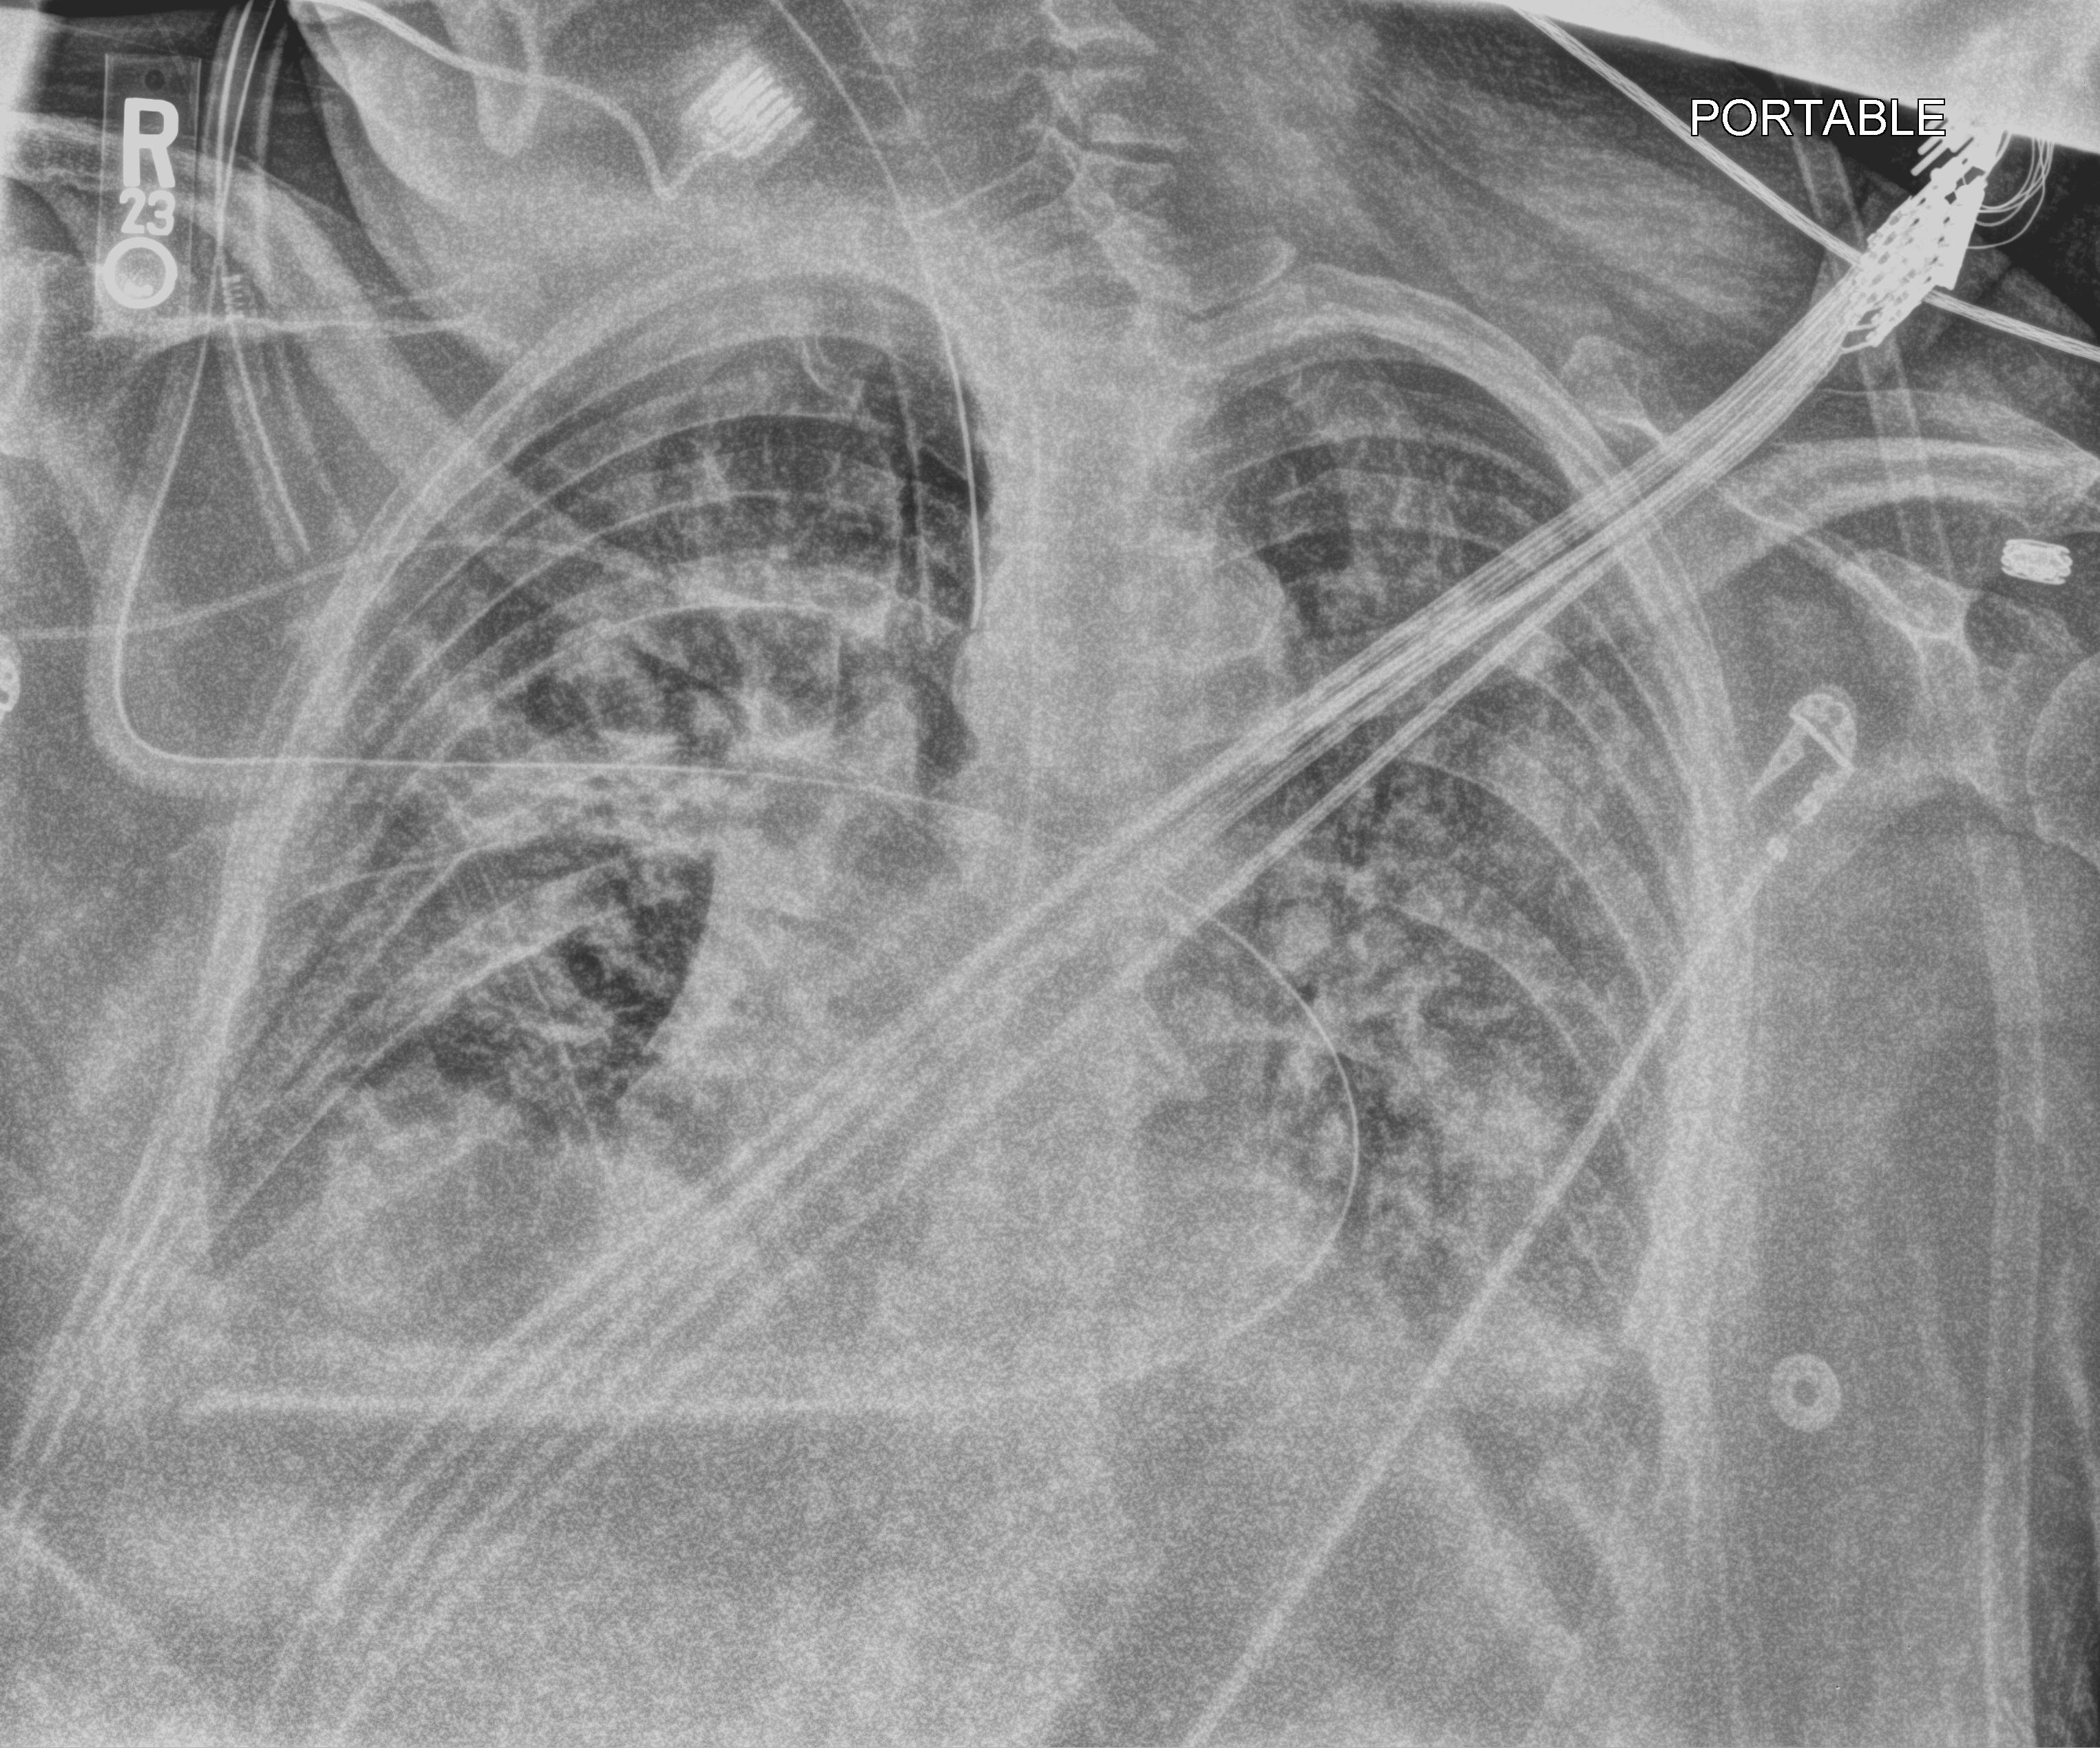
Chest X-ray (portable), anteroposterior (AP) projection. Patient hospitalised with COVID-19; male, aged 60–74 years.
Hospital-stay facts (about this admission, not read from this image; timing relative to this image not recorded): diabetes (admission record): no; mechanically ventilated during this hospital stay: yes.